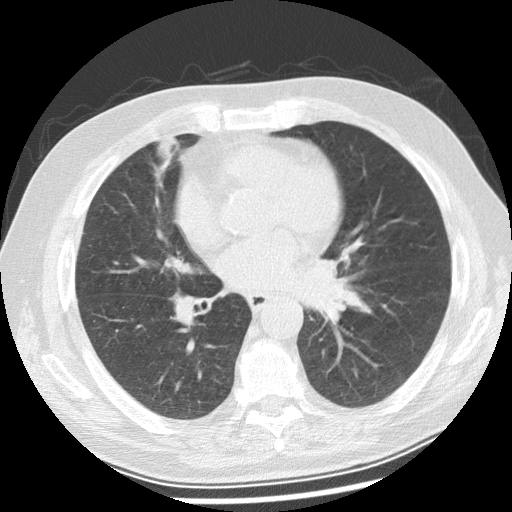
Low-dose screening chest CT, one axial slice; position 124 of 250 along the scan axis; reconstruction kernel STANDARD; 120 kVp; lung window (W 1500 / L -600 HU); 512 × 512 image matrix, field of view 360 × 360 mm.
Outlined on this slice (outlined manually by an expert reader):
- lesion 1 (tumor, left main bronchus): bounding box [x1, y1, x2, y2] px = [293, 259, 350, 323]